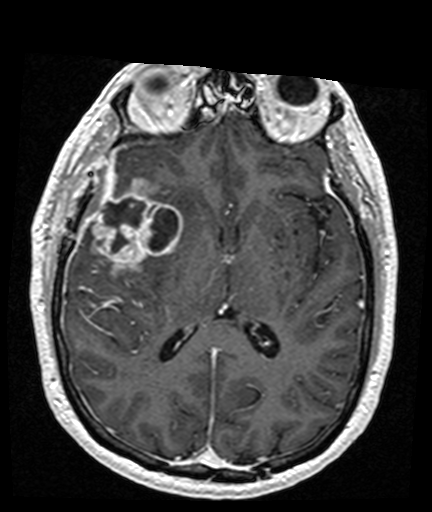
Brain MRI from a brain-tumour surgery series, one axial slice. Position 81 of 176 along the scan axis. T1-weighted post-contrast. 1 mm slice thickness. 432 × 512 image matrix. From the clinical record (not read from this slice): histopathology: Glioblastoma; WHO grade: 4; IDH mutation: no; tumour location: Right Frontal Temporal, Posterior Sylvian Fissure.
Outlined on this slice (manually delineated by an expert):
- tumour: bounding box (x1, y1, x2, y2) in pixels: (90, 178, 183, 276)